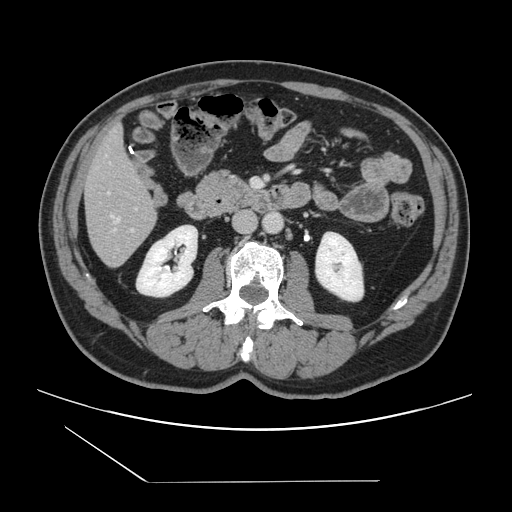
Contrast-enhanced abdominal CT, one axial slice; slice 43 of 157 in the series (ordered by position); 120 kVp; intravenous contrast given; soft-tissue window (W 400 / L 40 HU); 2.5 mm slice thickness; 512 × 512 image matrix, field of view 407 × 407 mm. Male patient, age 61 years. Case-level facts recorded for this patient, not image findings: diagnosis: colorectal cancer liver metastases, imaged before liver resection; multiple liver metastases: yes; largest metastasis: 5.5 cm; disease in both lobes: yes.
Structures marked on this image (expert manual segmentation):
- hepatic veins: bounding box <113,216,120,230> (left, top, right, bottom; pixels)
- liver: <85,129,157,266>
- planned liver remnant (the part of the liver to remain after resection): <85,129,154,219>
- portal vein (with intrahepatic branches): <132,228,134,231>